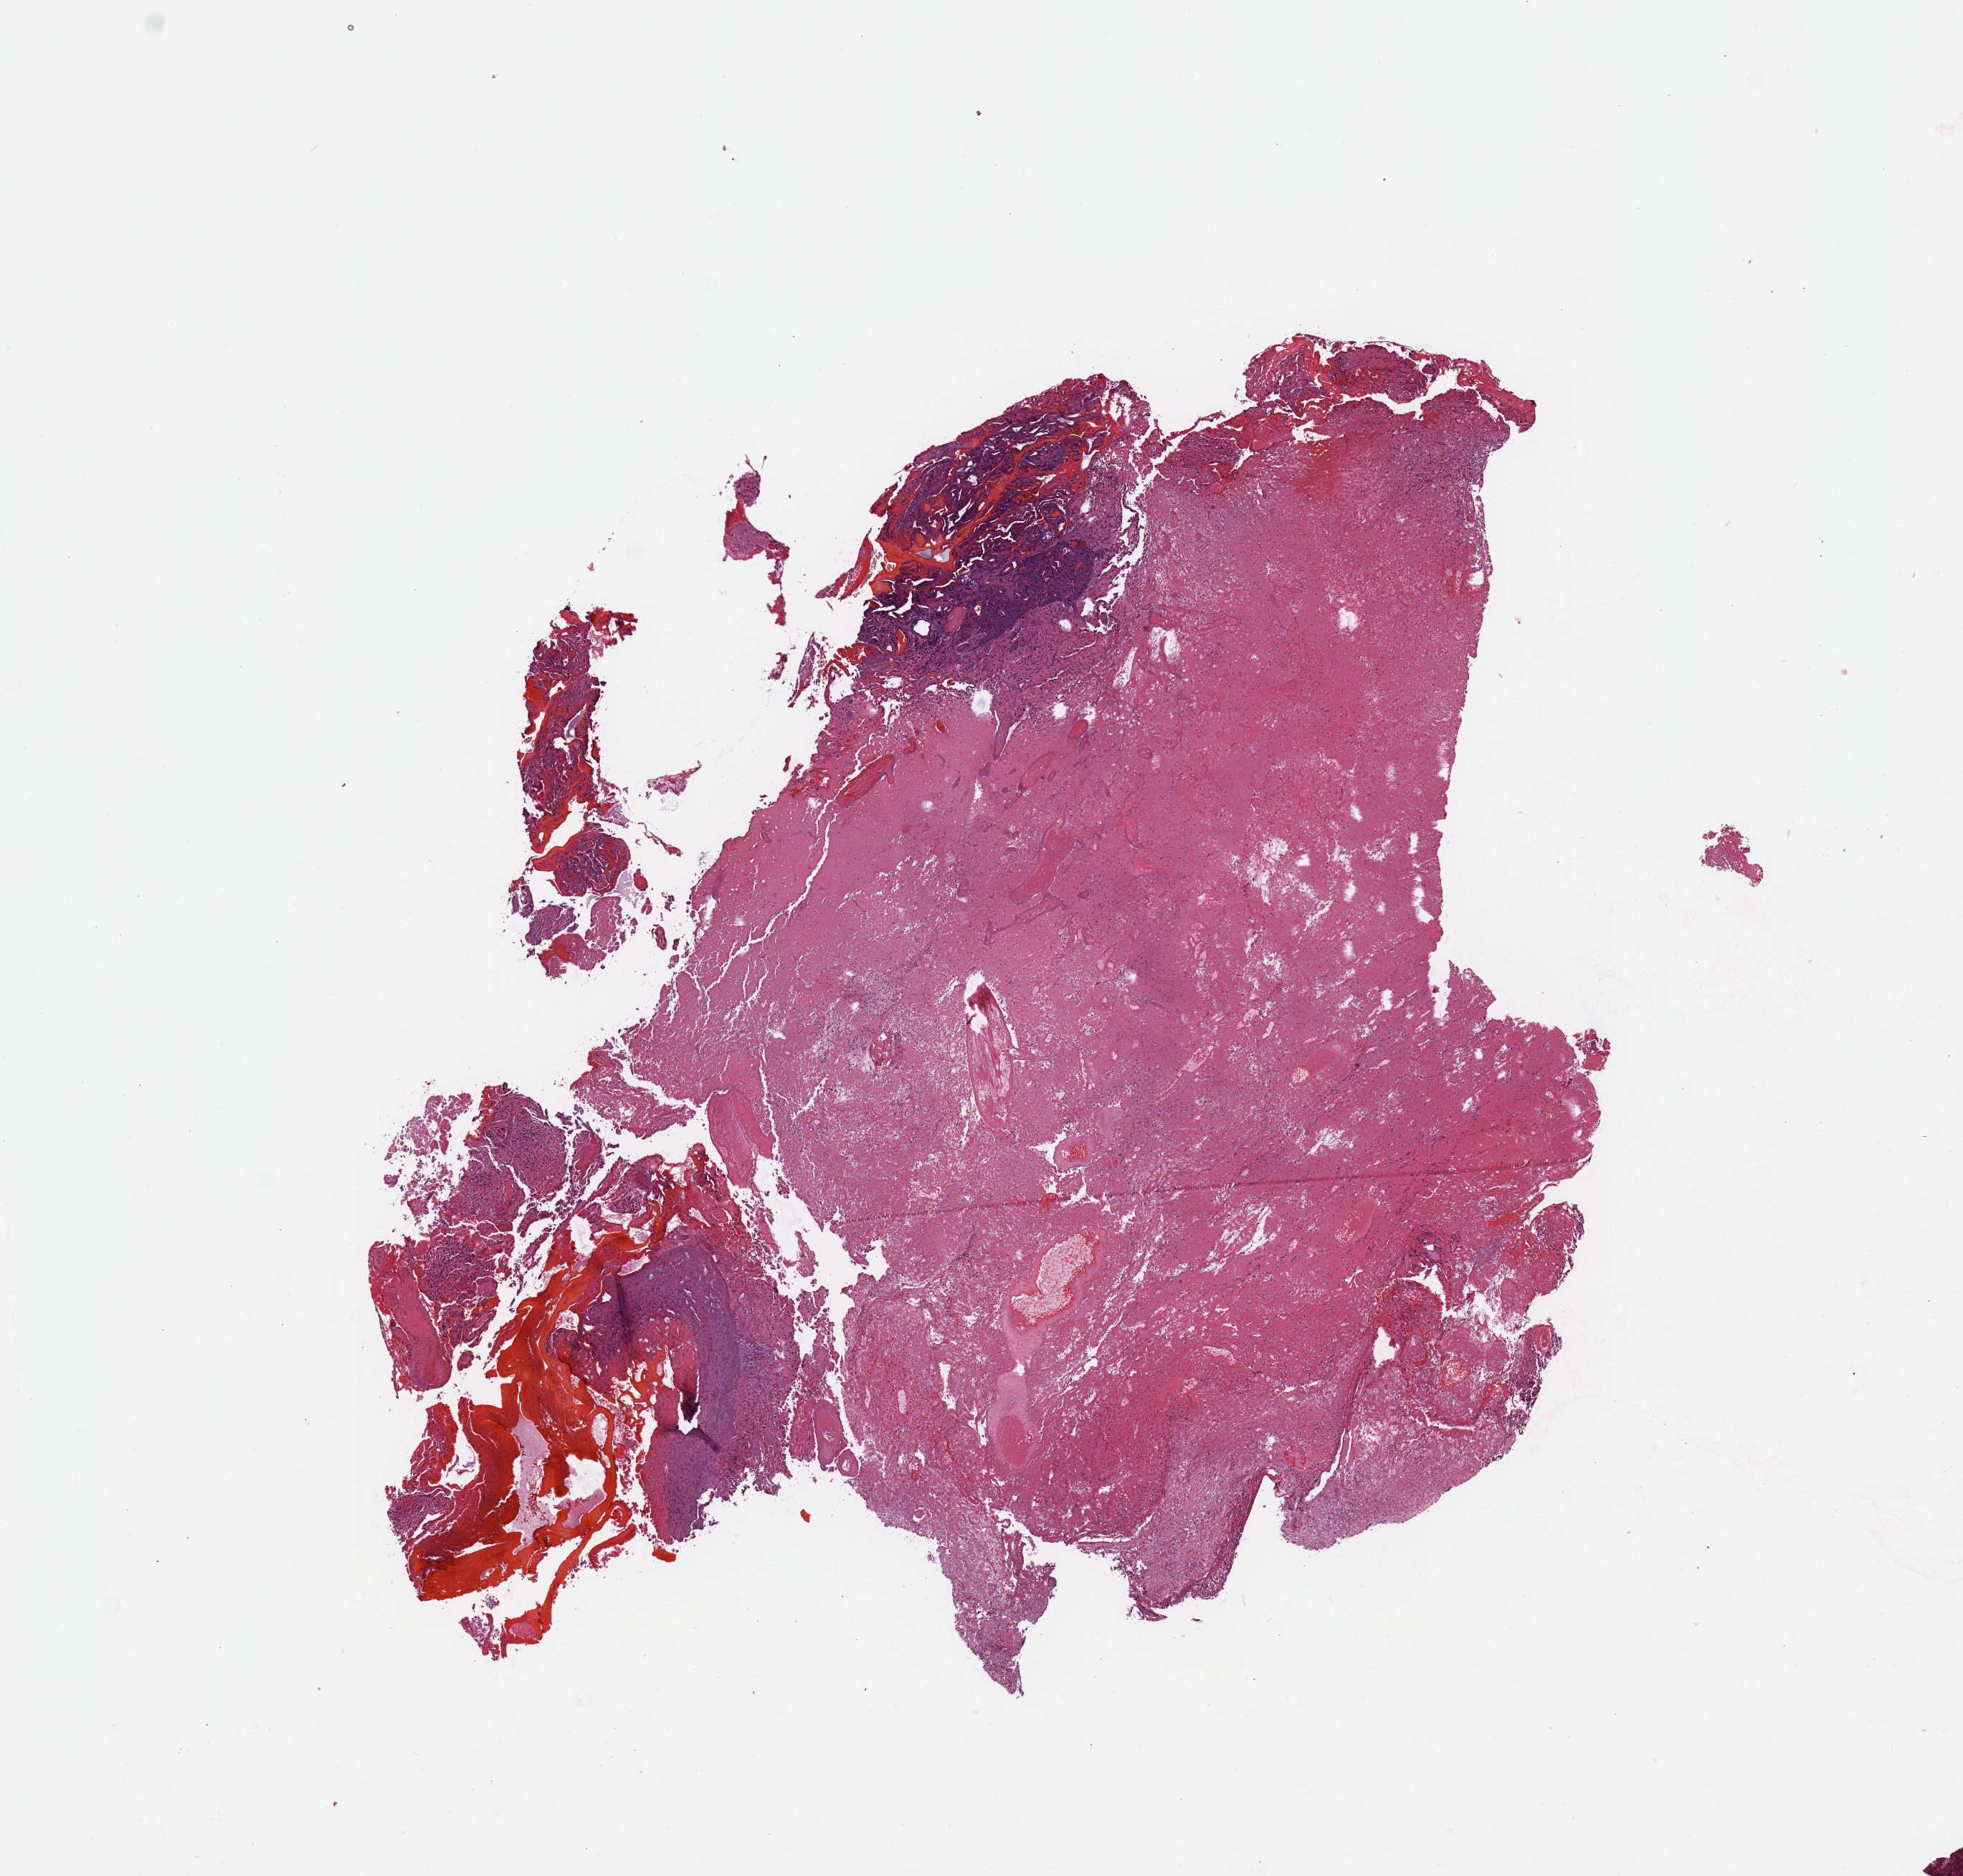
Digitized H&E tissue section (whole slide), low-resolution overview of the scanned area, about 10.8 x 10.3 mm, tumour tissue sample, brain. Patient: male, age 45 years.
Diagnosis: Glioblastoma.